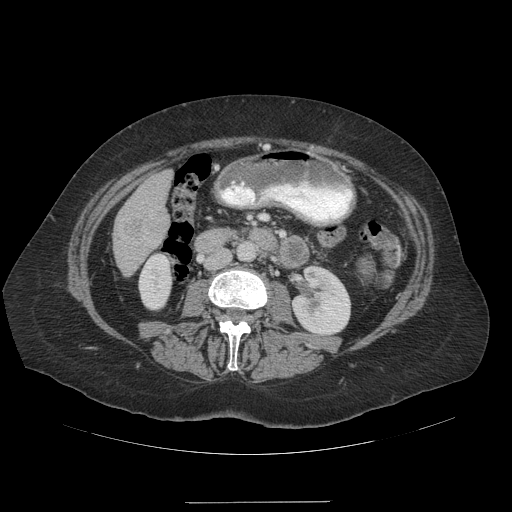
Contrast-enhanced abdominal CT (liver protocol), one axial slice. Slice 38 of 99 in the series (ordered by position). Reconstruction kernel STANDARD. 140 kVp. Soft-tissue window (W 400 / L 40 HU). 2.5 mm slice thickness. 512 × 512 image matrix, field of view 440 × 440 mm. From the clinical record (not read from this slice): diagnosis: hepatocellular carcinoma (patient treated with transarterial chemoembolisation; whether this scan precedes or follows treatment is not stated here); TNM stage (as recorded): Stage-IVA.
Outlined on this slice (semi-automatically segmented with operator editing):
- liver parenchyma outside the tumour (the mass and vessels are separate outlines, so this box may not span the whole liver): bounding box [x1, y1, x2, y2] px = [114, 170, 172, 274]